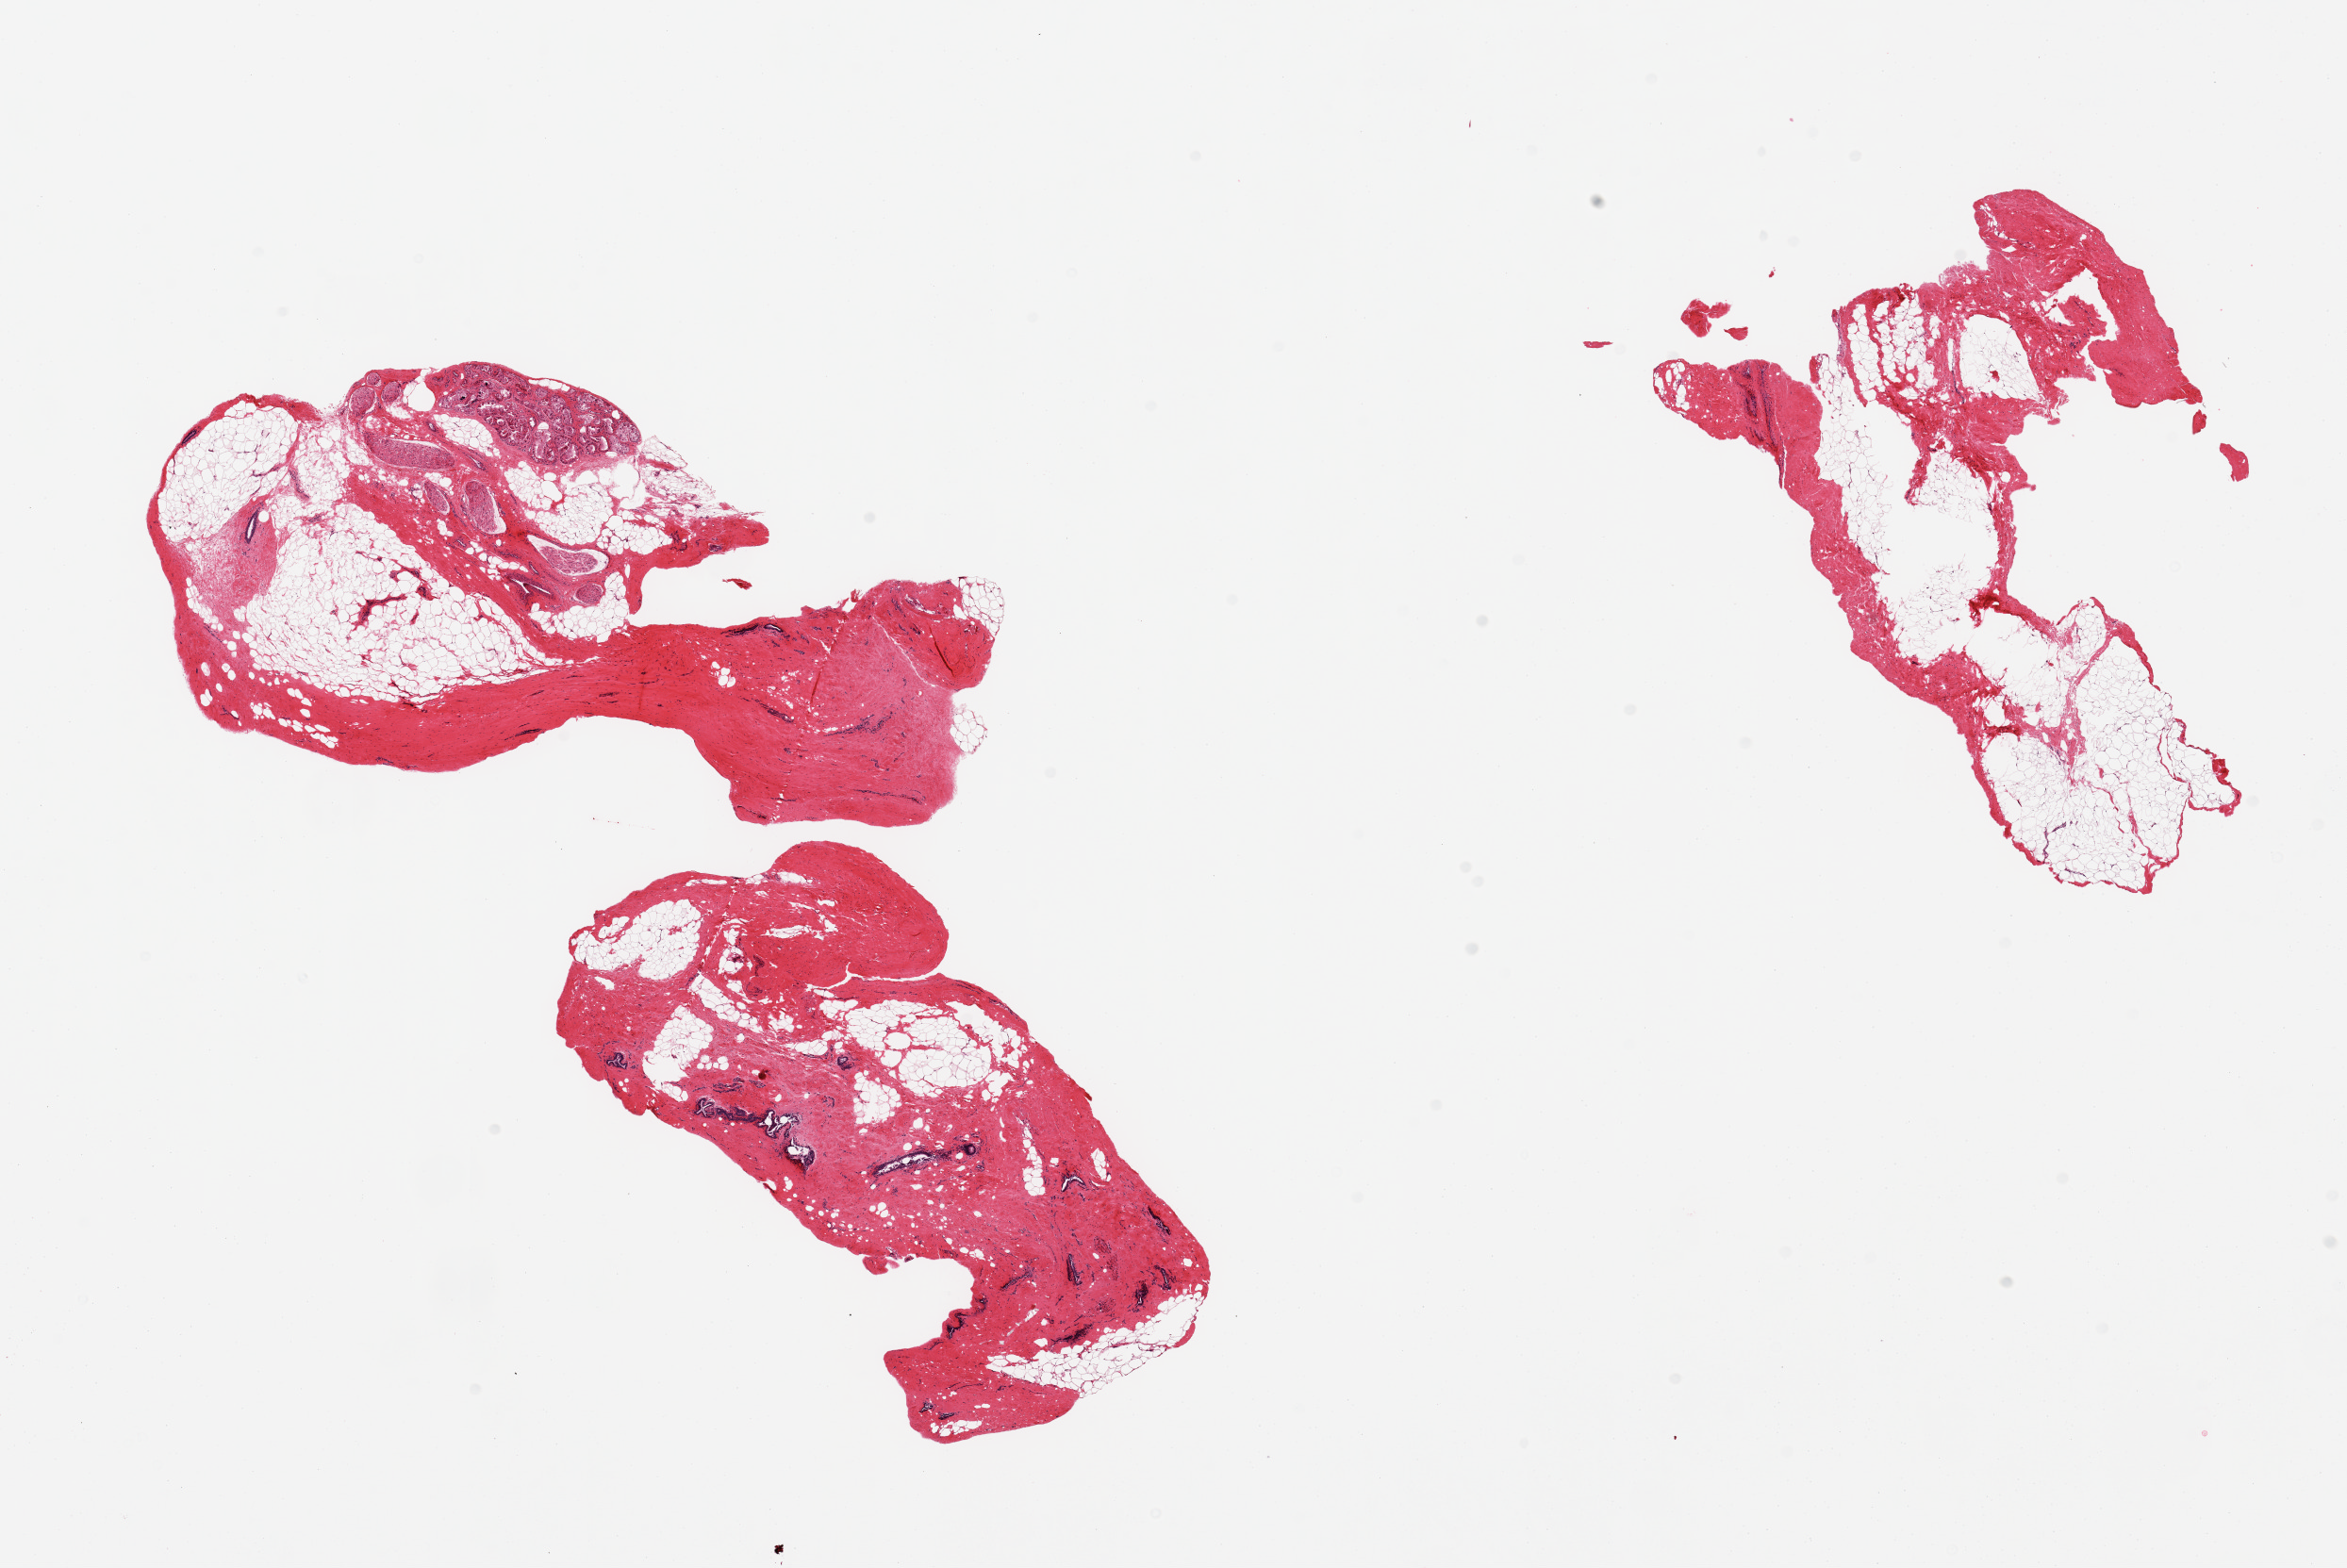
Haematoxylin and eosin whole-slide image — shown as a low-resolution overview of the whole scanned area (about 19.7 x 13.2 mm, acquisition: 20x scan); PAXgene-fixed paraffin-embedded (PFPE) section; target tissue: breast; donor tissue sample. Donor: male.
- reviewer comment on this tissue sample: 2 pieces; 1 piece has mammary ducts and dense stroma with gynecomastoid features; small focus of apocrine glands; other piece is fibrofatty tissue without mammary elements